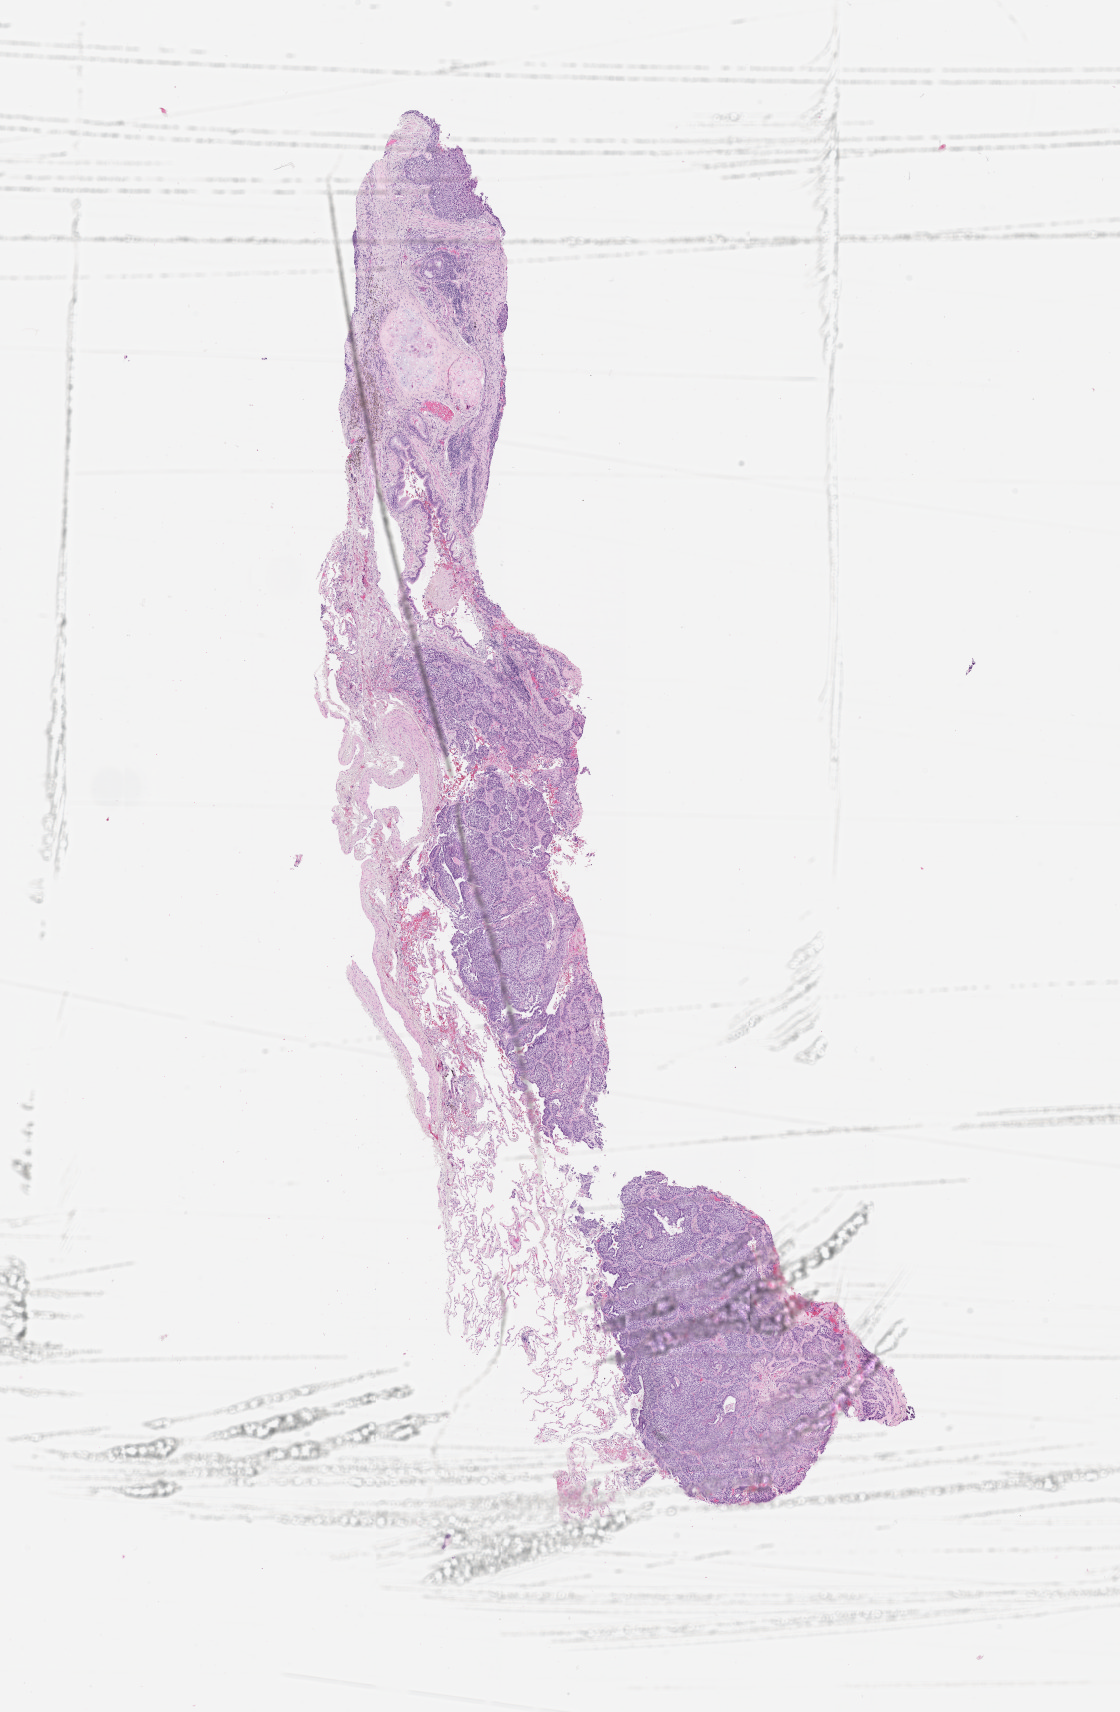
Digitized H&E-stained tissue section (whole slide) — low-resolution overview of the scanned area, about 9.0 x 13.8 mm, tumour tissue sample, lung. Patient: female, age 69 years.
Patient diagnosis (cohort enrolment): squamous cell carcinoma (lung).